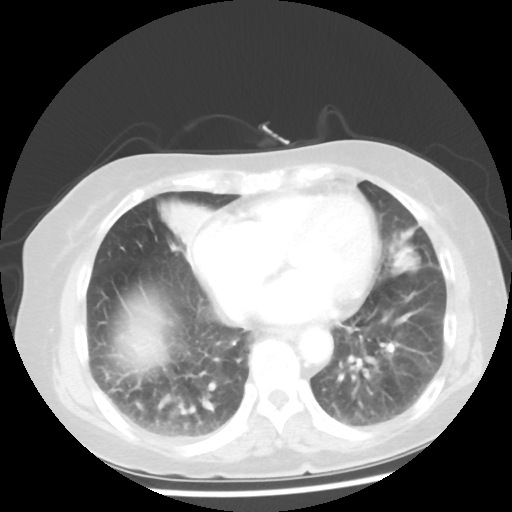
Chest CT, one axial slice. Position 15 of 50 along the scan axis. Reconstruction kernel STANDARD. Lung window (W 1500 / L -600 HU). 512 × 512 image matrix, field of view 332 × 332 mm. Female patient, age 77 years. Case-level facts recorded for this patient, not image findings: clinical TNM (as recorded): T2 N3 M1a.
Structures marked on this image (rectangle marked by the reading radiologist):
- lung tumour (recorded histology: adenocarcinoma): bounding box (x1, y1, x2, y2) in pixels: (383, 221, 425, 280)